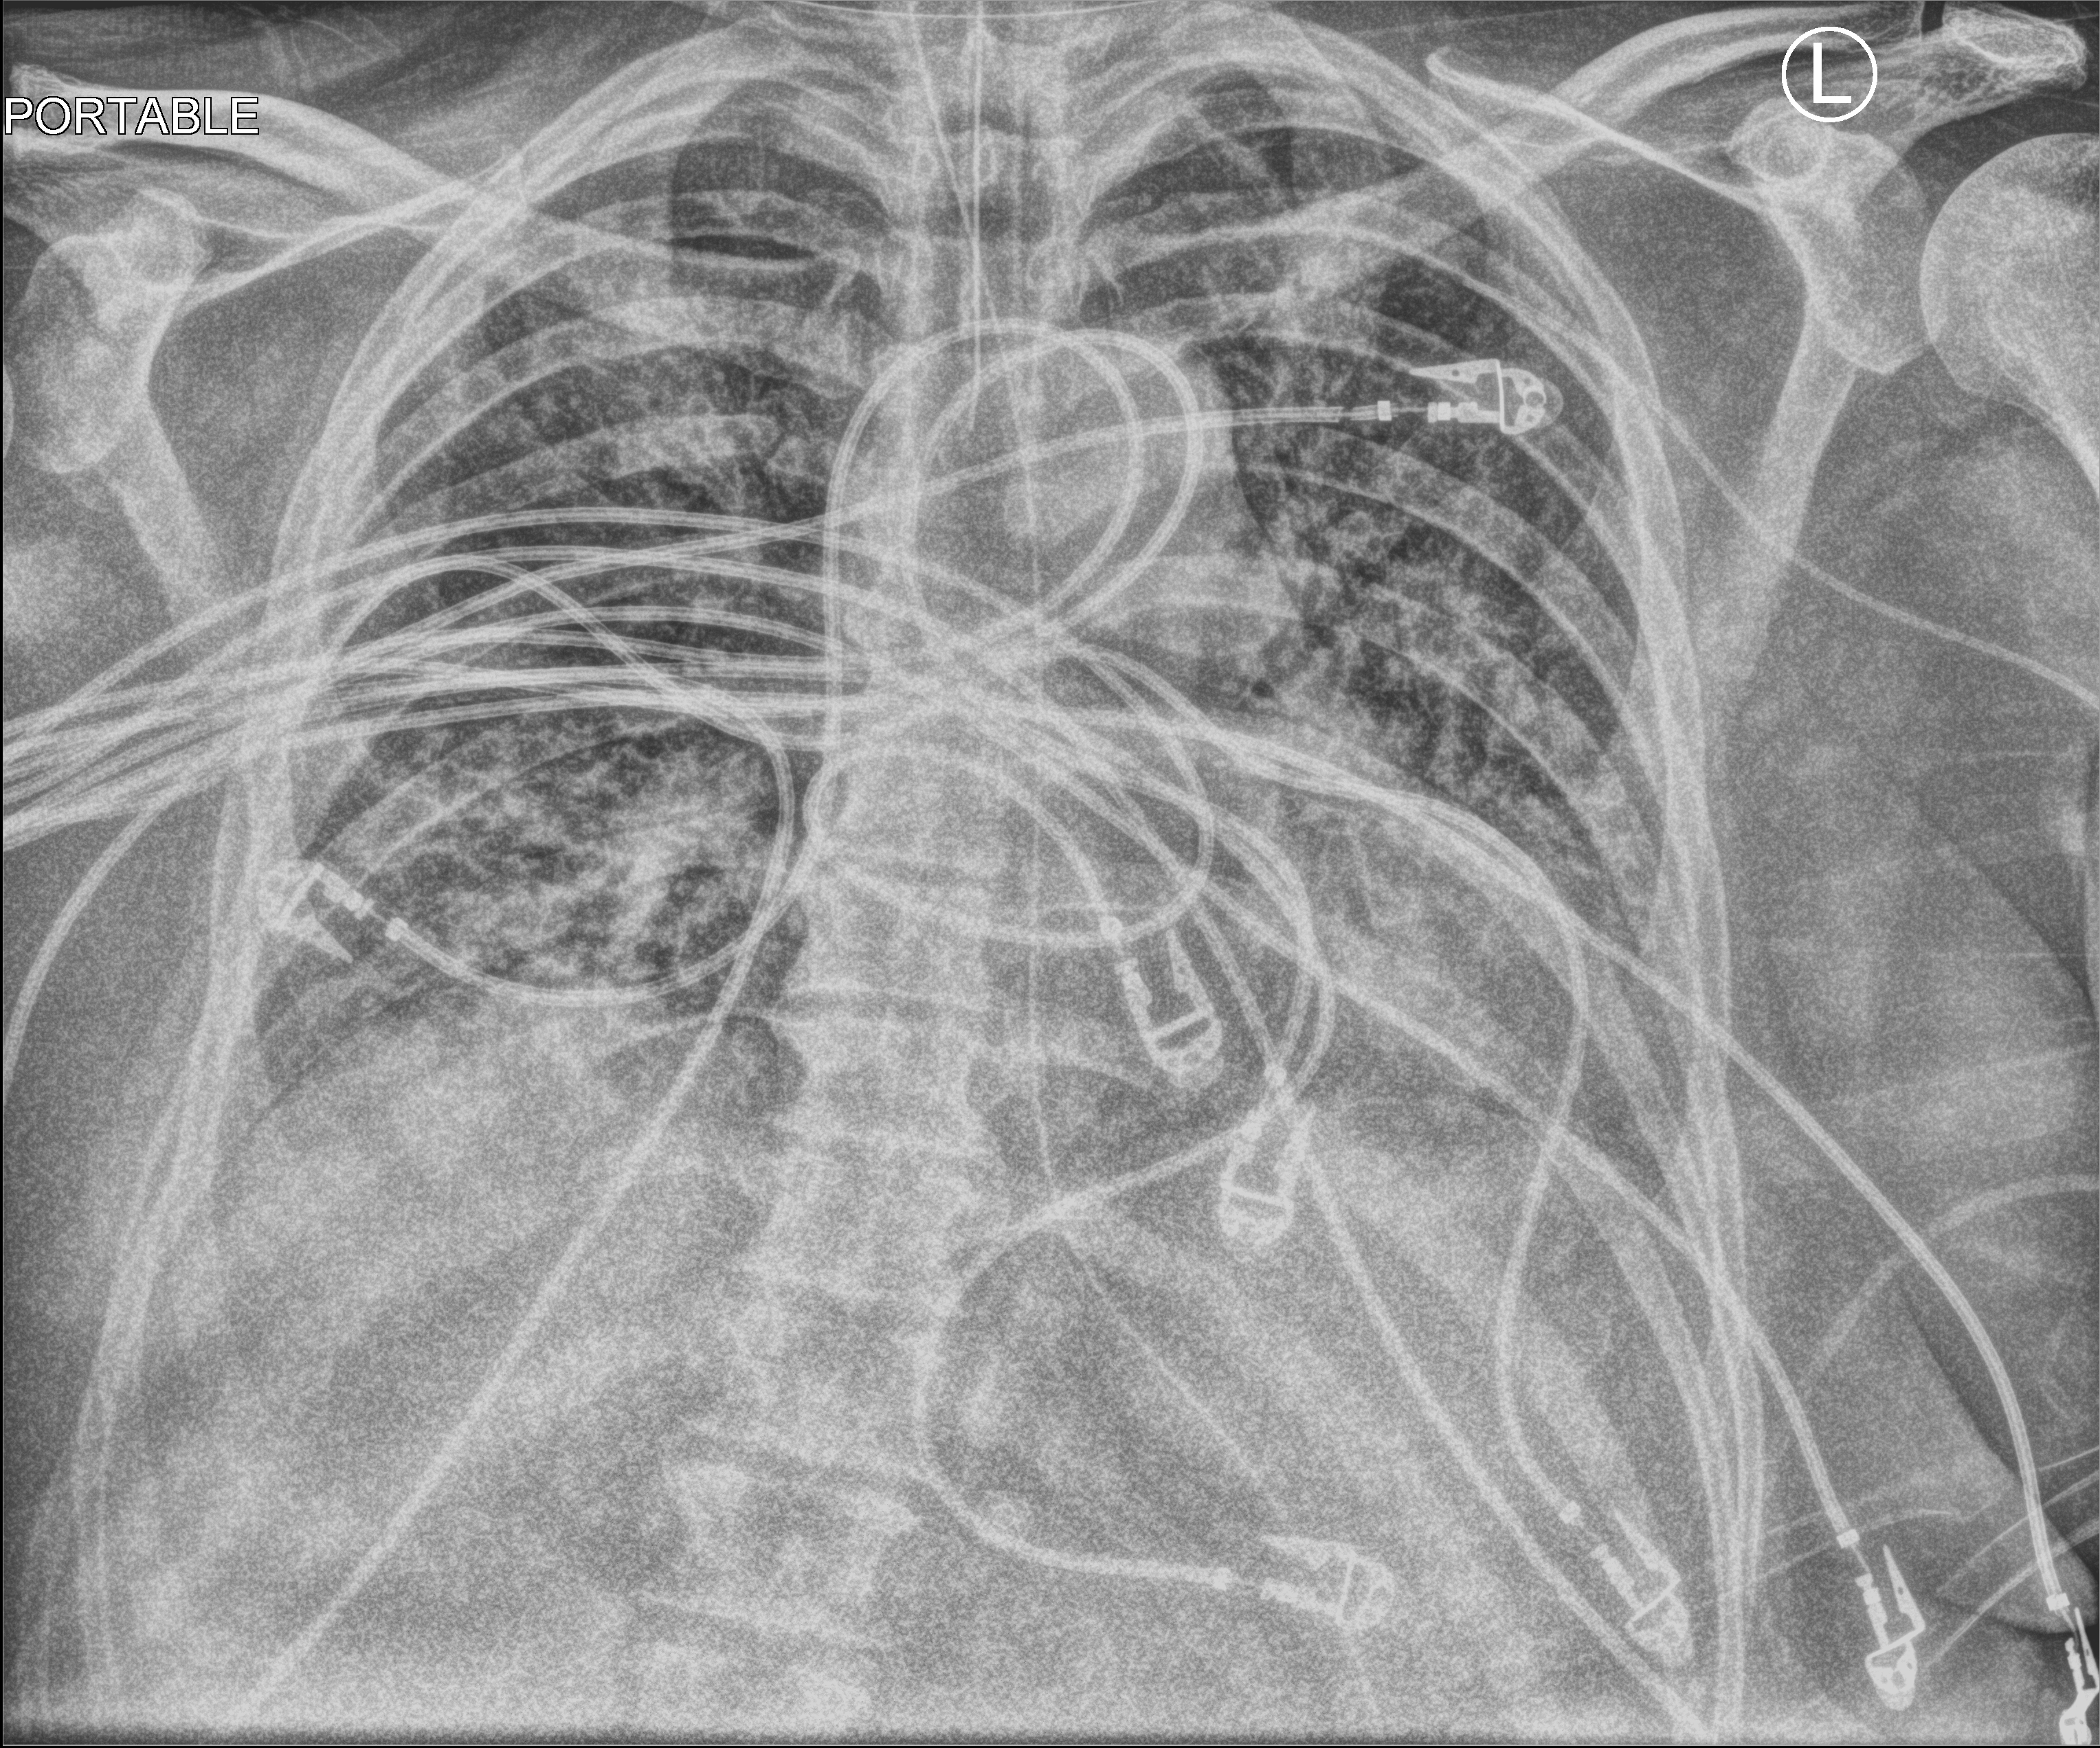
Portable chest radiograph, anteroposterior (AP) projection. Patient hospitalised with COVID-19; male, aged 60–74 years.
Admission-level facts for this patient (not findings on this image; timing relative to this image not recorded): diabetes (admission record): no; mechanically ventilated during this hospital stay: yes; admitted to intensive care during this hospital stay: yes.